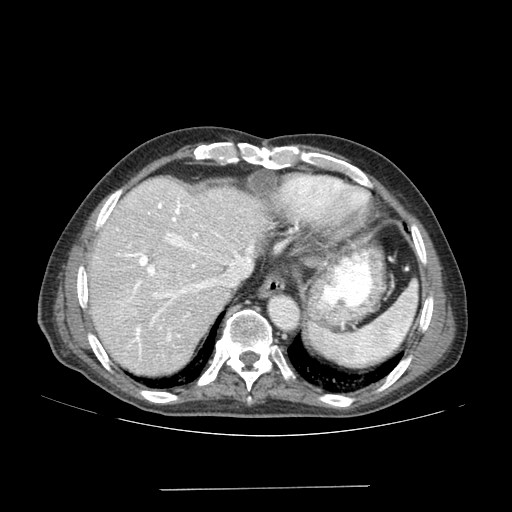
Contrast-enhanced abdominal CT (liver protocol), one axial slice; 120 kVp; soft-tissue window (W 400 / L 40 HU); 512 × 512 image matrix, field of view 400 × 400 mm. Case-level facts recorded for this patient, not image findings: diagnosis: hepatocellular carcinoma (patient treated with transarterial chemoembolisation; whether this scan precedes or follows treatment is not stated here); TNM stage (as recorded): Stage-IVA; Child-Pugh class: A; tumour differentiation: poorly differentiated; tumour nodularity: uninodular.
Annotated regions visible in this slice (semi-automatically segmented with operator editing):
- liver parenchyma outside the tumour (the mass and vessels are separate outlines, so this box may not span the whole liver): box from (x=88, y=177) to (x=270, y=376) px
- mass: (x=153, y=263)–(x=183, y=293)
- liver vessels: (x=117, y=201)–(x=253, y=353)